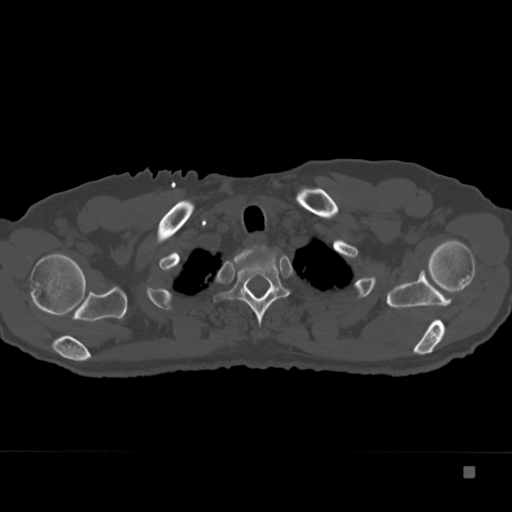
CT including the spine, one axial slice; position 303 of 332 along the scan axis; reconstruction kernel Br40s; 120 kVp; bone window (W 1800 / L 400 HU); 1.5 mm slice thickness; 512 × 512 image matrix, field of view 389 × 389 mm. Male patient, age 72 years. Case-level facts recorded for this patient, not image findings: primary cancer: skeletal.
Annotated regions visible in this slice (semi-automatically segmented with operator editing):
- T1 vertebra: box from (x=234, y=249) to (x=253, y=263) px
- T2 vertebra: (x=213, y=246)–(x=290, y=327)
- T3 vertebra: (x=247, y=283)–(x=271, y=293)